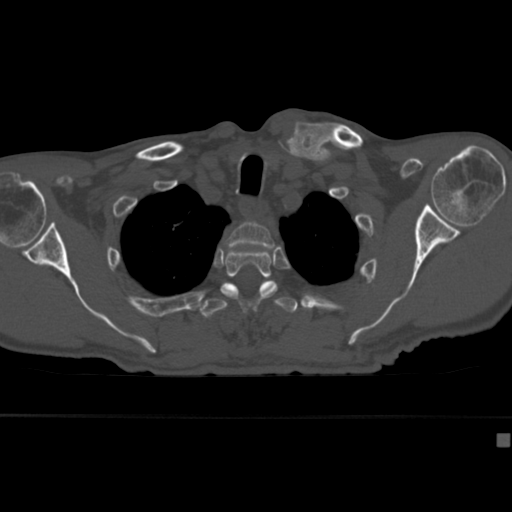
CT including the spine, one axial slice; slice 331 of 430 in the series (ordered by position); reconstruction kernel Br40s; 120 kVp; bone window (W 1800 / L 400 HU); 1.5 mm slice thickness; 512 × 512 image matrix, field of view 337 × 337 mm. Patient: male, 64 years. Case-level facts recorded for this patient, not image findings: primary cancer: uterus; vertebrae with lytic lesions (as recorded): T1, T4, T5, T7, L5.
Outlined on this slice (semi-automatic segmentation, software-assisted and operator-edited):
- T2 vertebra: bounding box <223,222,275,261> (left, top, right, bottom; pixels)
- T3 vertebra: <222,249,278,290>
- T4 vertebra: <201,285,298,318>